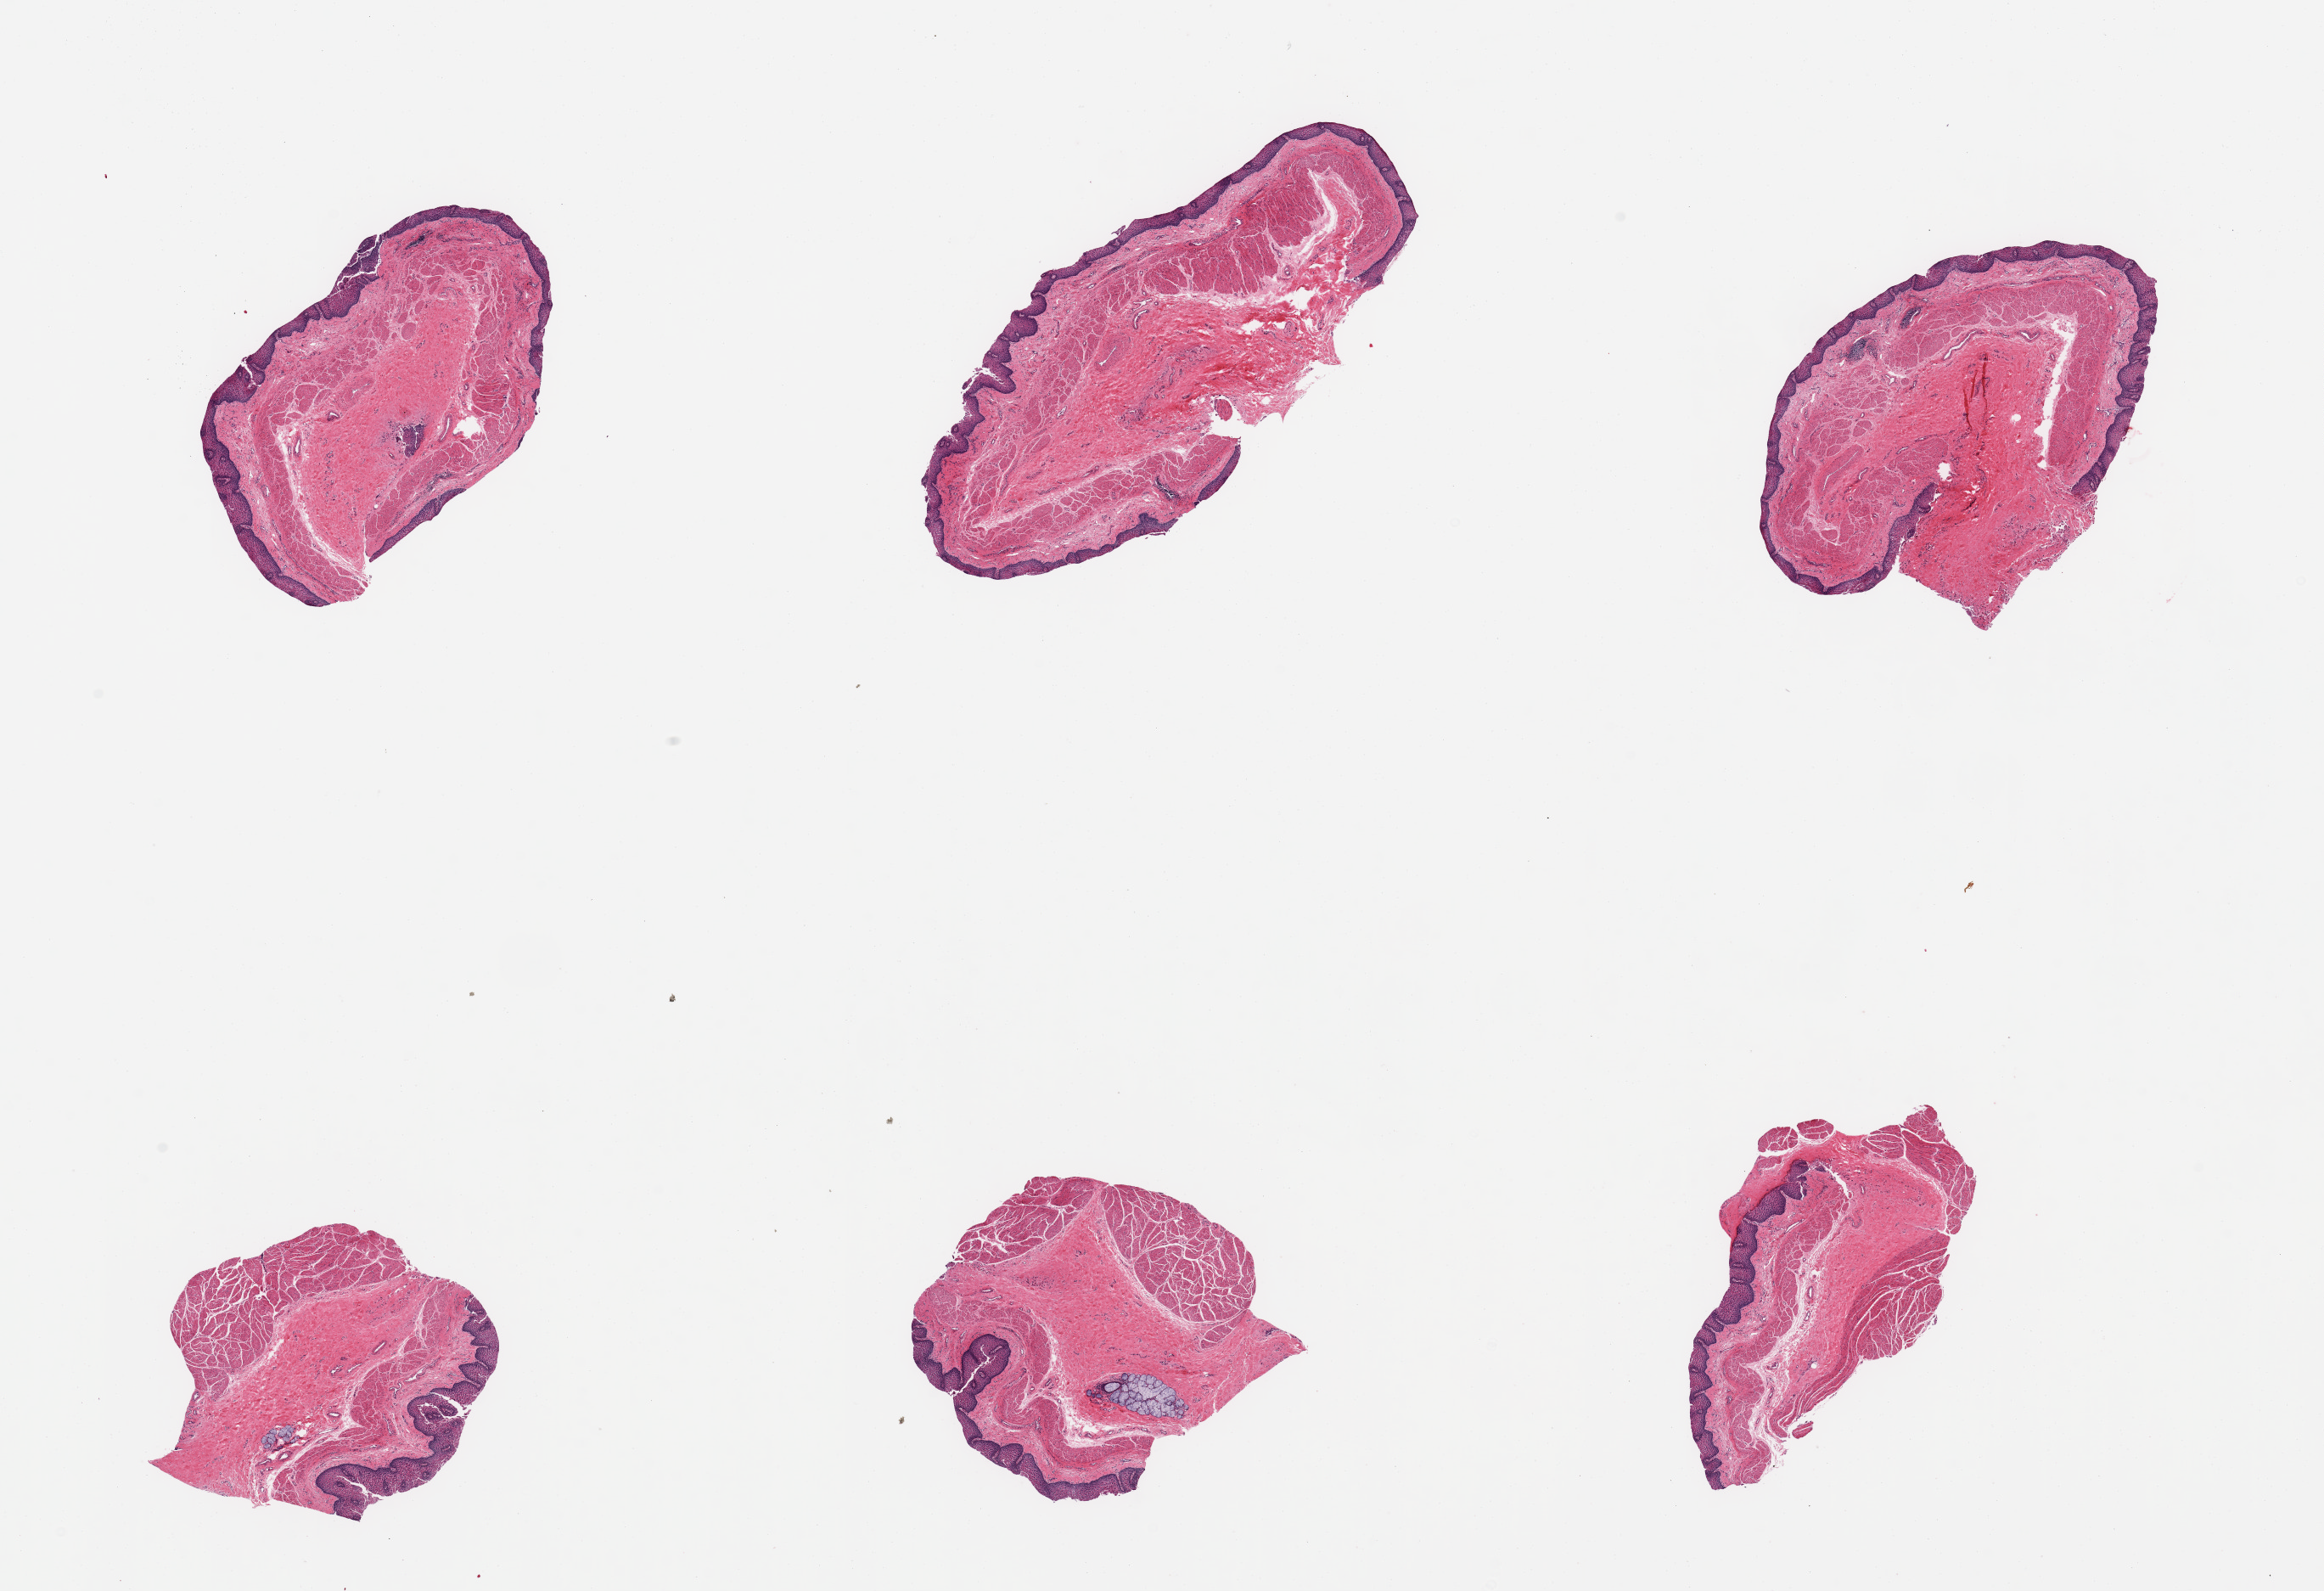
H&E whole-slide image, shown as a low-resolution overview of the whole scanned area (about 21.7 x 14.8 mm), PAXgene-fixed, paraffin-embedded tissue, section of esophageal mucous membrane (target tissue), donor tissue sample. Donor: female.
Reviewer comment on this tissue sample: 6 pieces; stratified squamous epithelium, submucosa with couple of glands and muscularis.